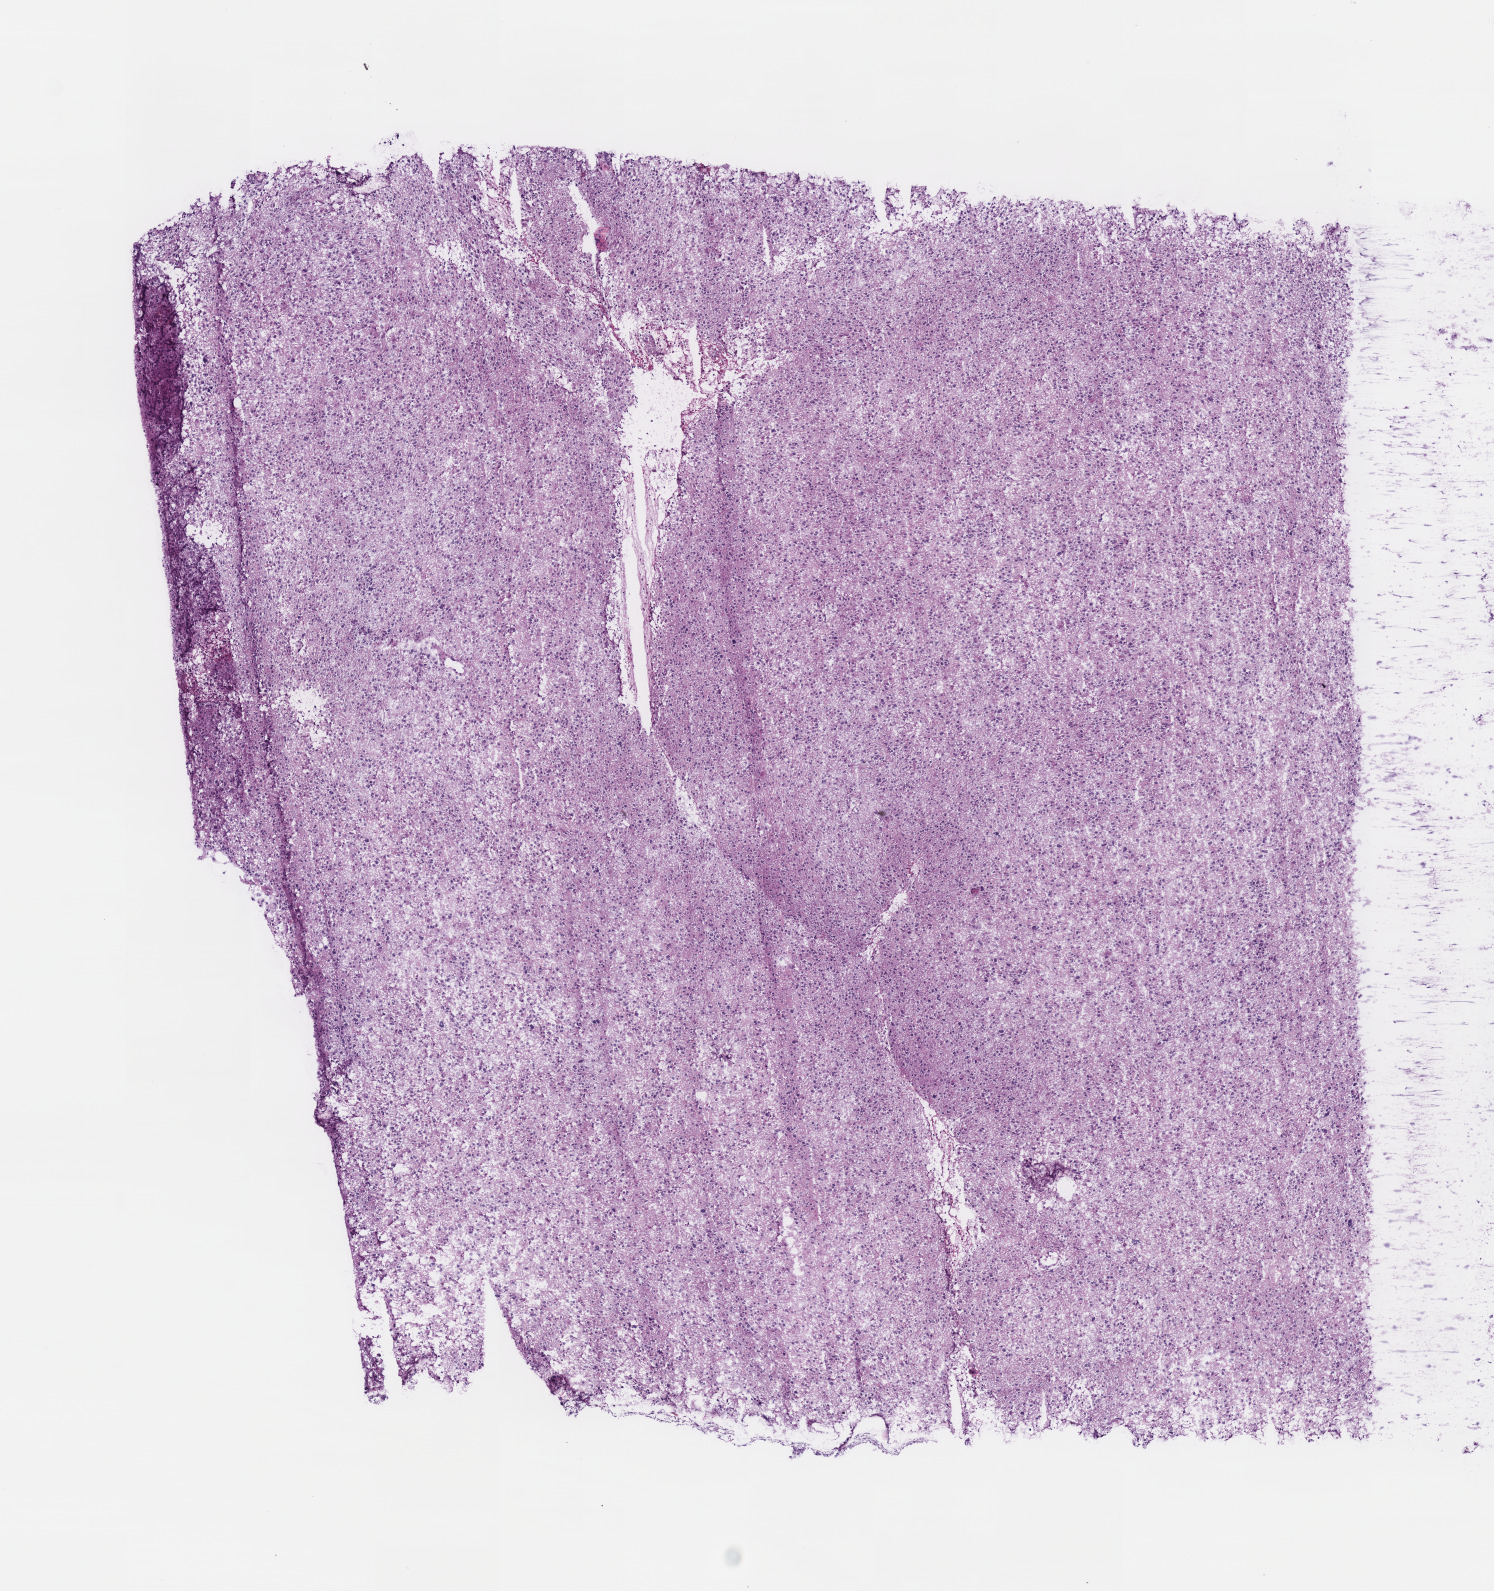
Whole-slide histology image, H&E-stained, whole scanned area (about 5.9 x 6.3 mm, from a 40x scan) shown as a low-resolution overview, frozen section from the top of the tissue portion, brain, primary tumour sample. Male, age 29 years at initial diagnosis. Histologic grade: G2 (moderately differentiated). Slide review estimates, as recorded: tumour cells 100%, tumour nuclei 80%, normal cells 0%, stromal cells 0%, necrosis 0%.
Diagnosis: Mixed glioma (cerebrum).